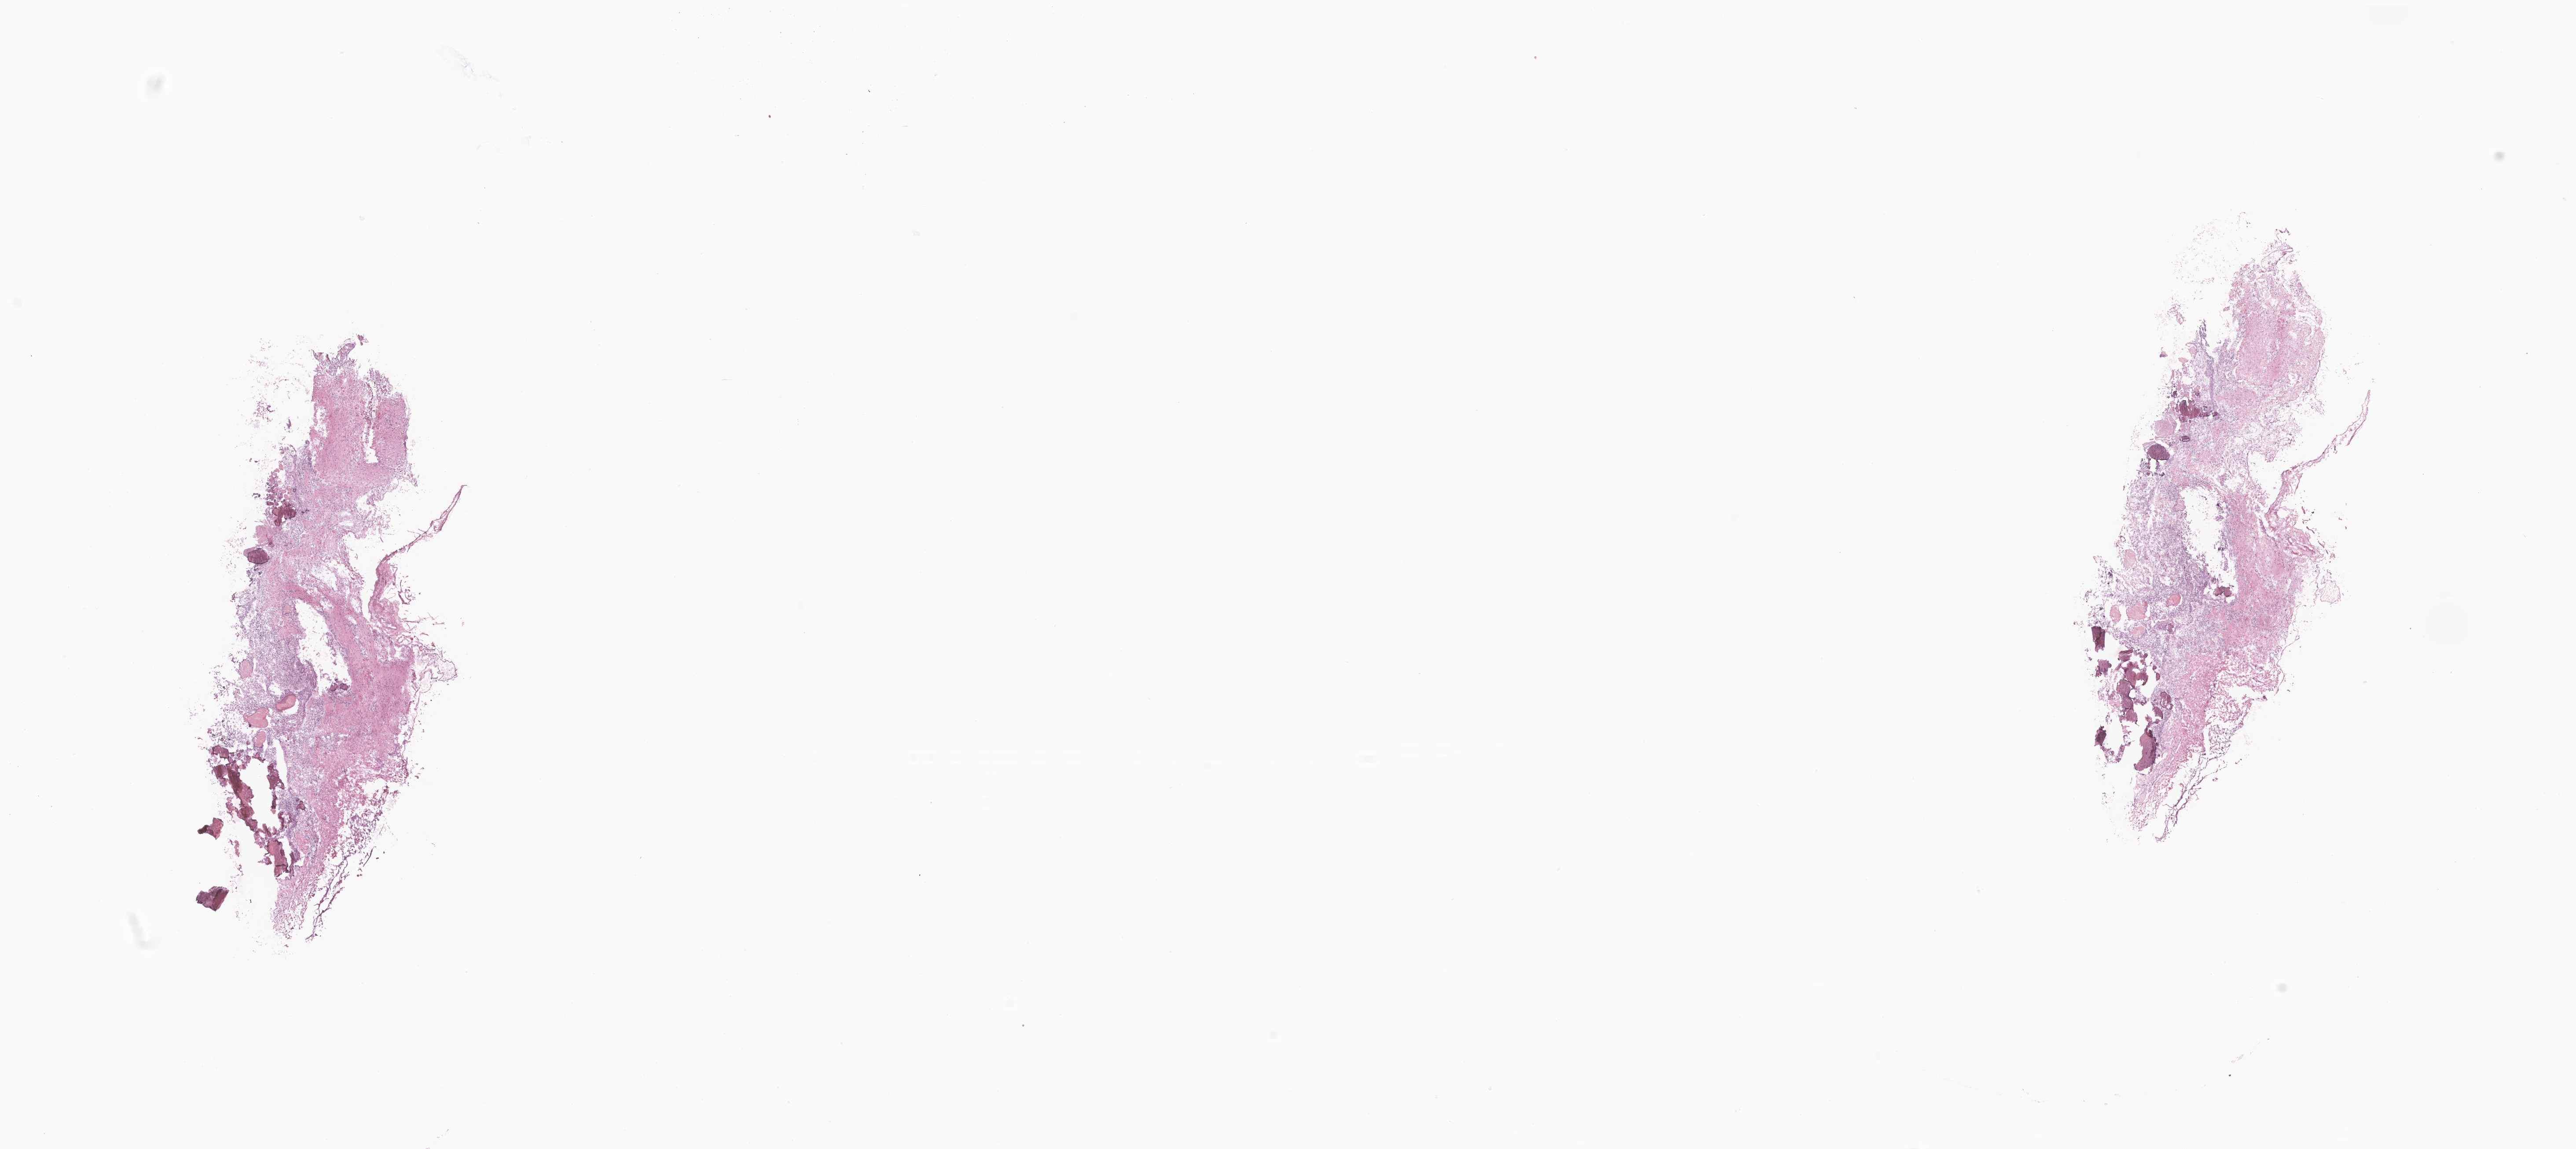
Digitized hematoxylin and eosin (H&E)-stained section of tumor tissue from the brain, shown as a low-resolution overview of the whole scanned area (about 24.7 x 11.0 mm); frozen section (OCT-embedded). Patient male; age 91 months (7 years 7 months).
Recorded diagnosis: Craniopharyngioma, adamantinomatous.